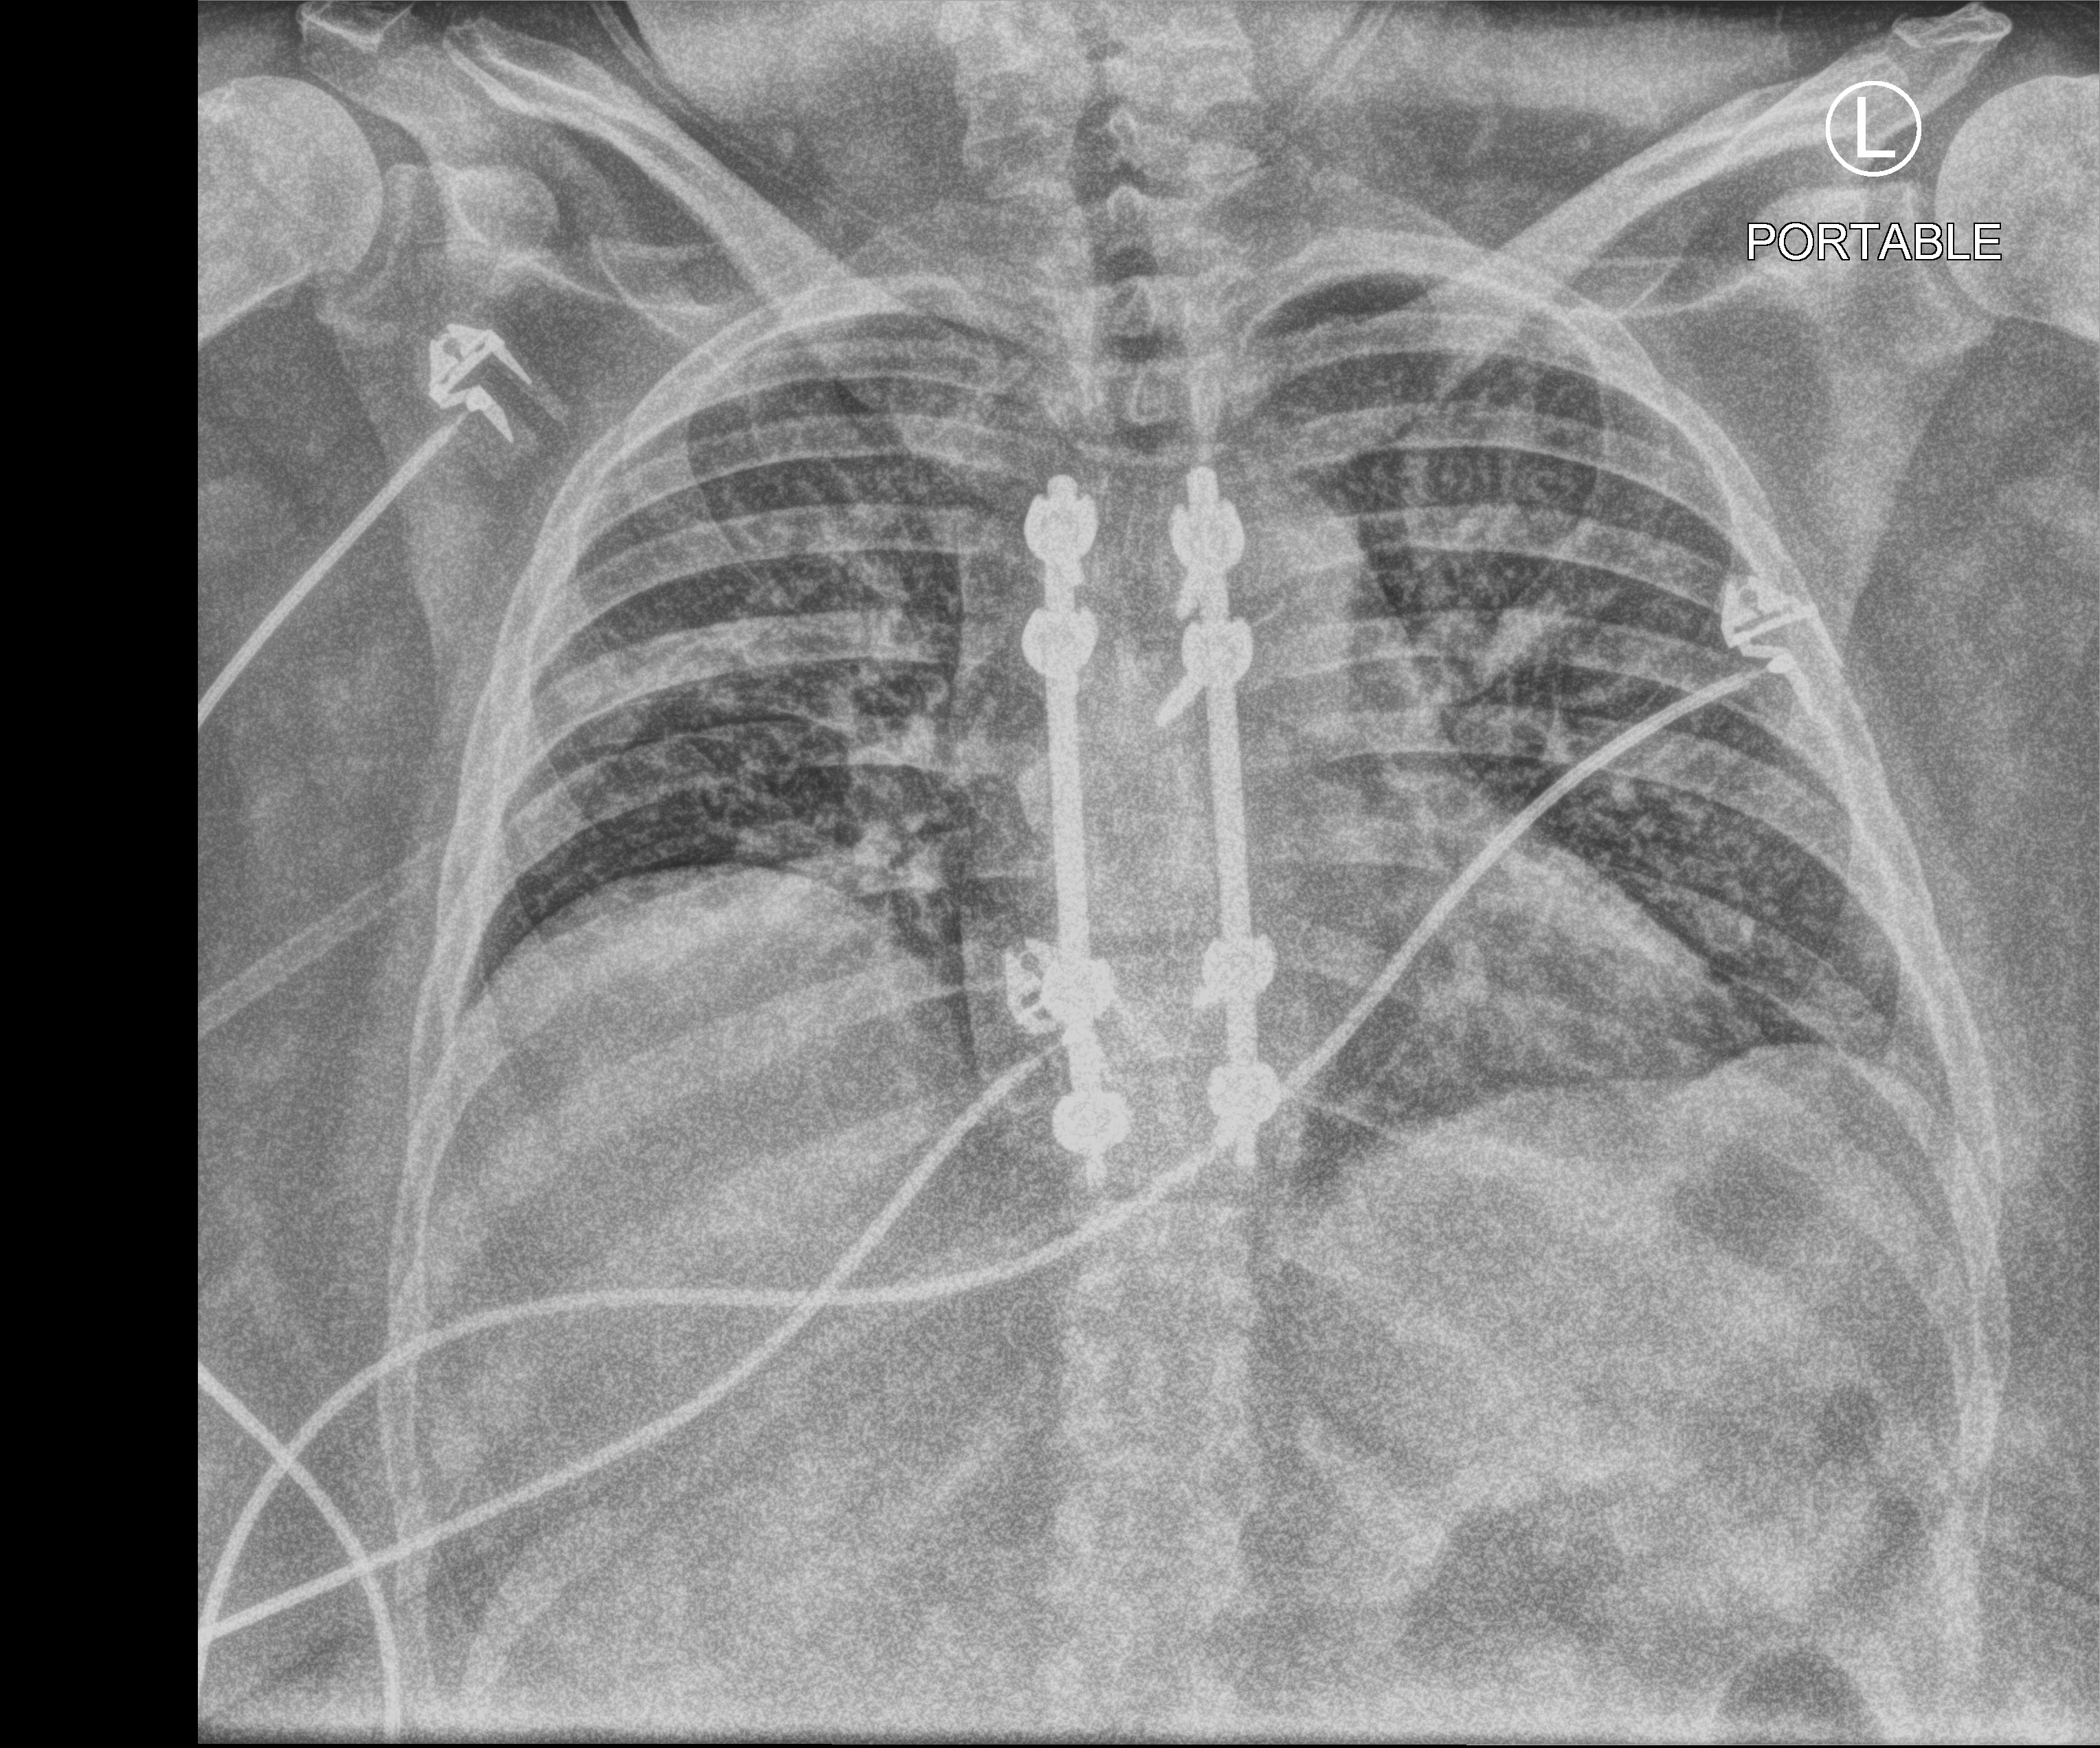
Bedside chest radiograph (computed radiography); anteroposterior (AP) projection. Female patient hospitalised with COVID-19, age 18–59 years.
Hospital-stay facts (about this admission, not read from this image; timing relative to this image not recorded): mechanically ventilated during this hospital stay: no; diabetes (admission record): yes.